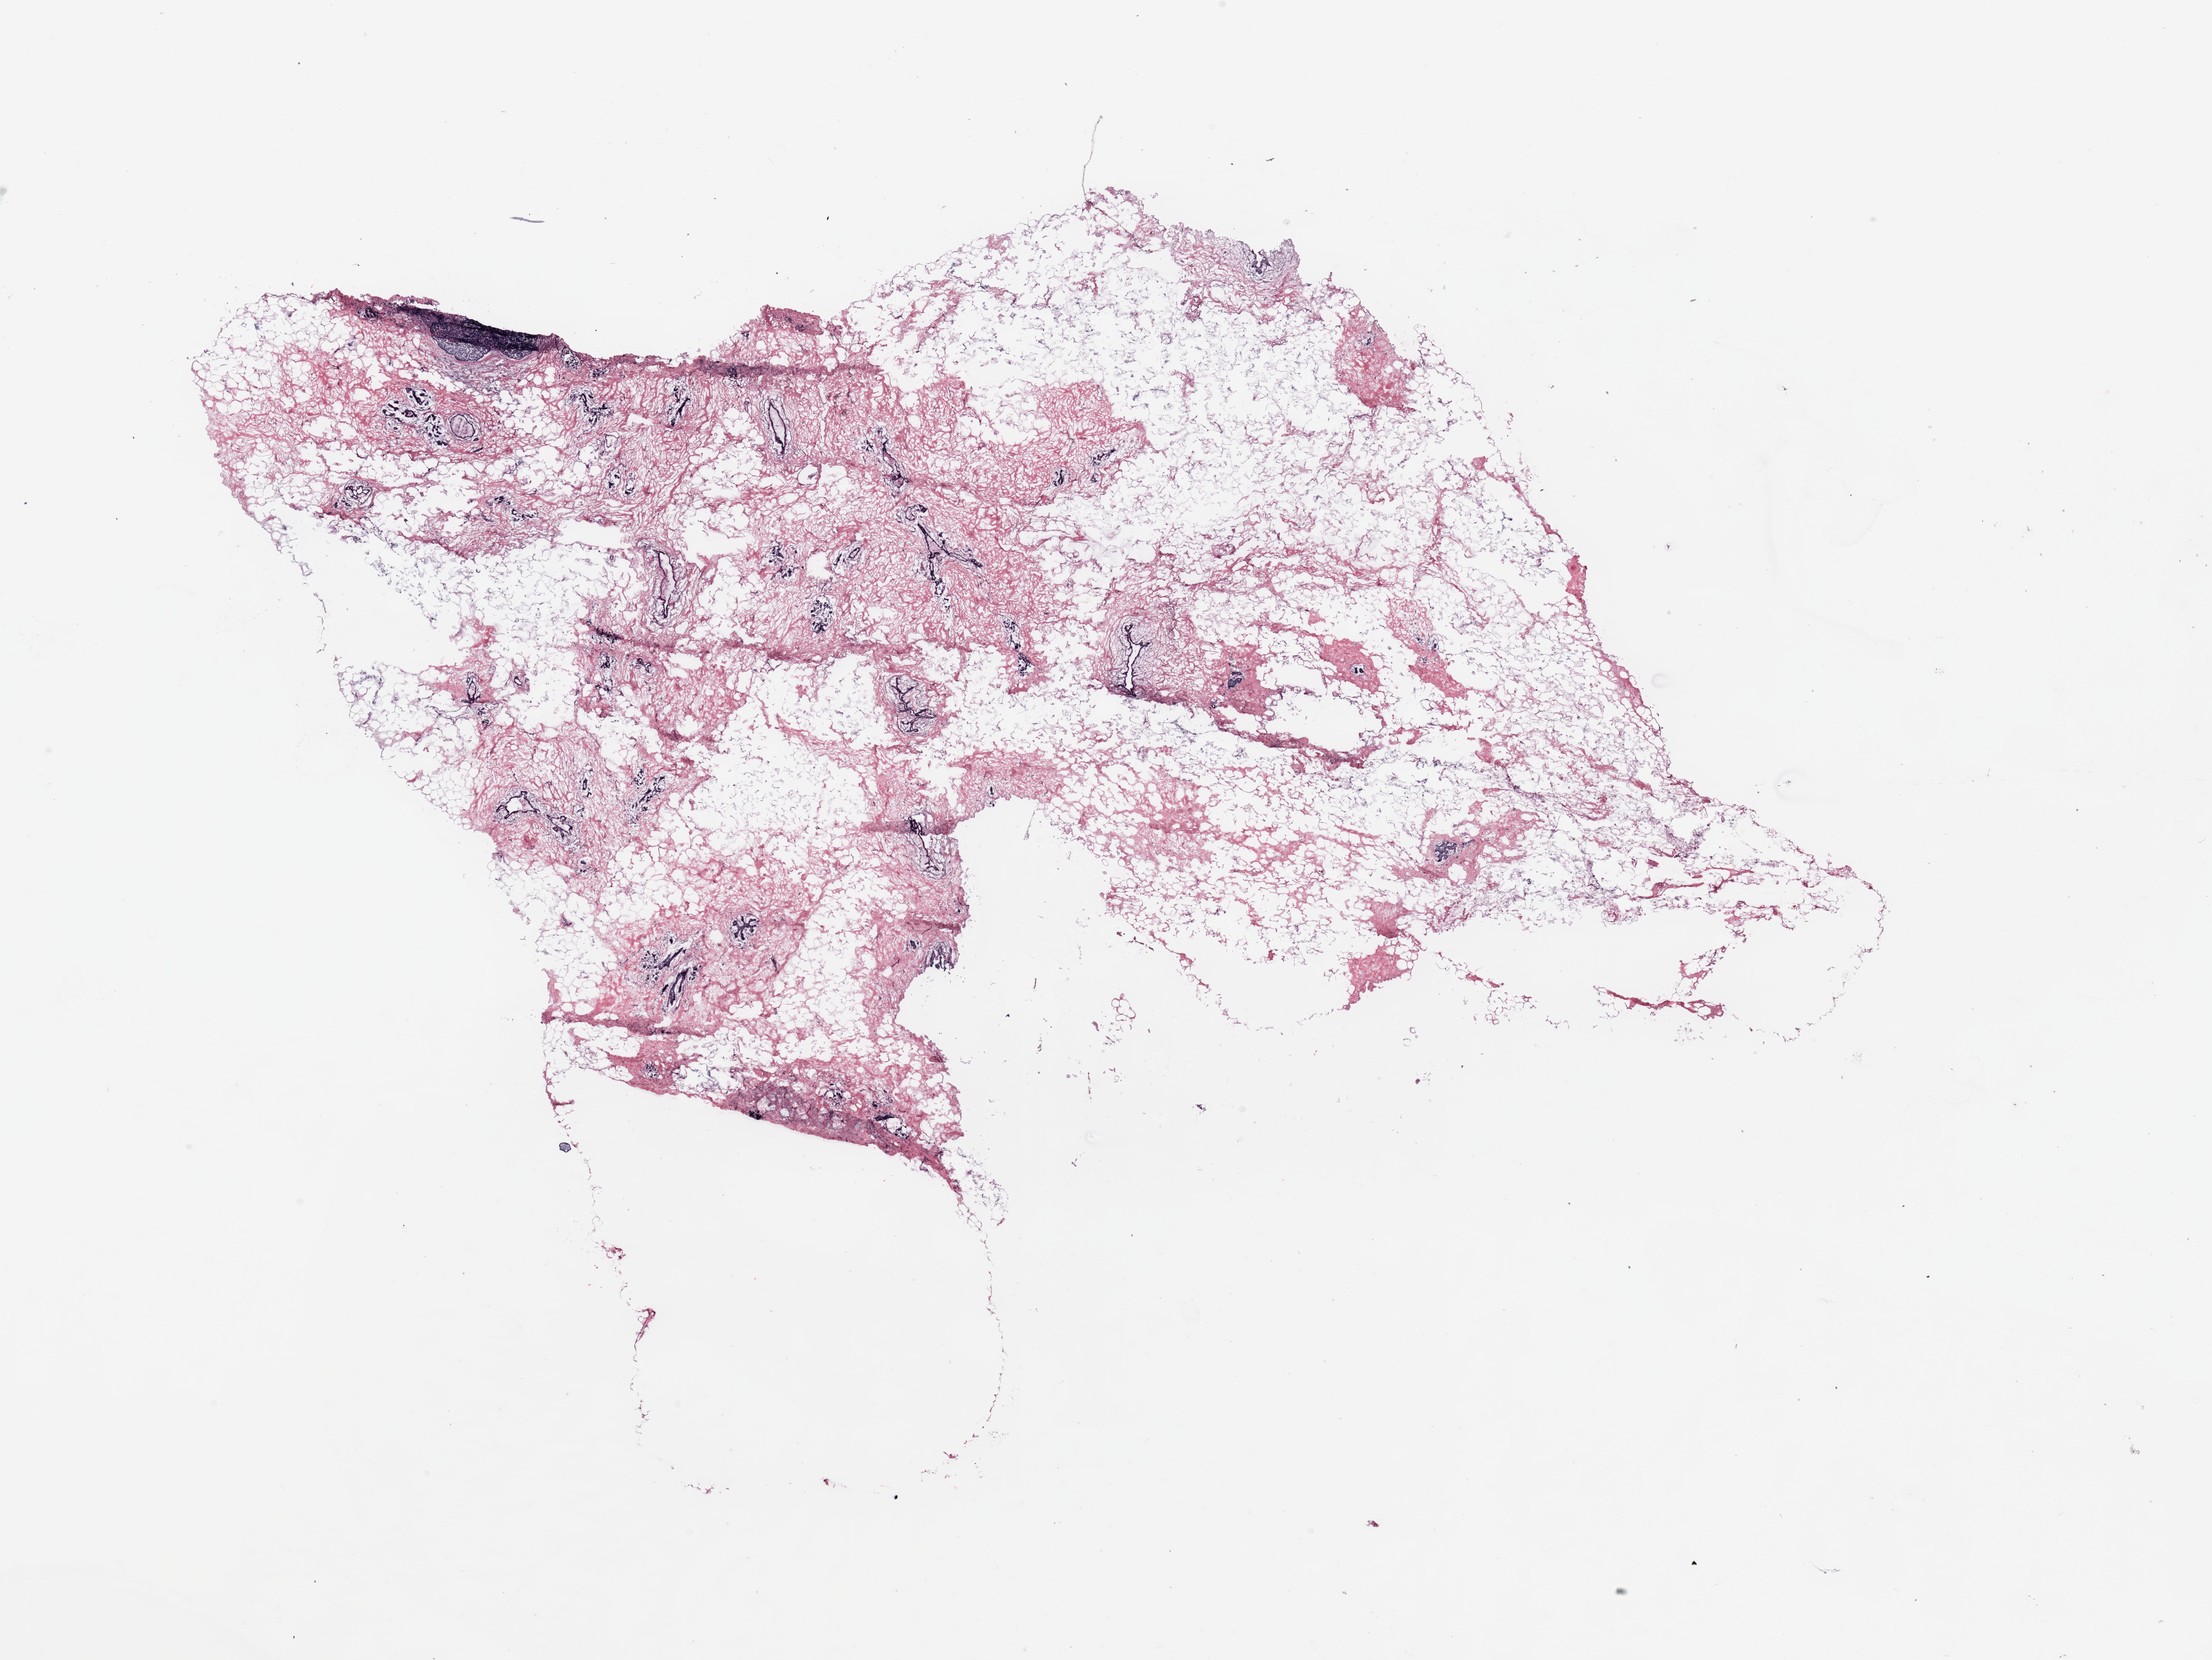
Whole-slide histology image, H&E-stained, low-resolution overview of the scanned area, about 25.6 x 19.2 mm. Breast, tumour tissue. Female, 54 y/o.
• histologic diagnosis: Infiltrating duct carcinoma, NOS
• AJCC pathologic stage: IIA